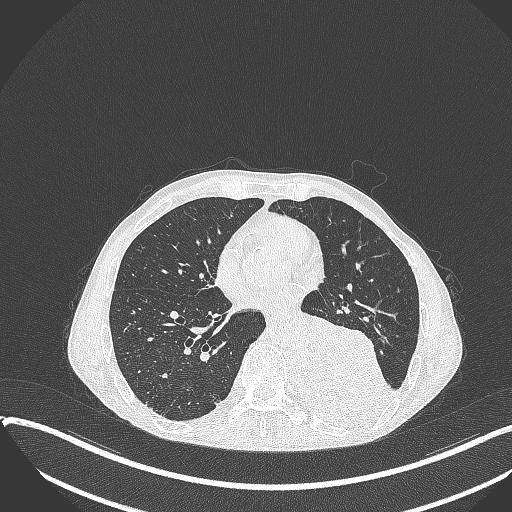
Chest CT, one axial slice. Slice 153 of 401 in the series (ordered by position). Lung window (W 1500 / L -600 HU). 1 mm slice thickness. 512 × 512 image matrix, field of view 400 × 400 mm. Patient: male, 57 years. Case-level facts recorded for this patient, not image findings: clinical TNM (as recorded): T4 N0 M0.
Annotated regions visible in this slice (rectangle marked by the reading radiologist):
- lung tumour (recorded histology: squamous cell carcinoma): box from (x=292, y=306) to (x=390, y=431) px